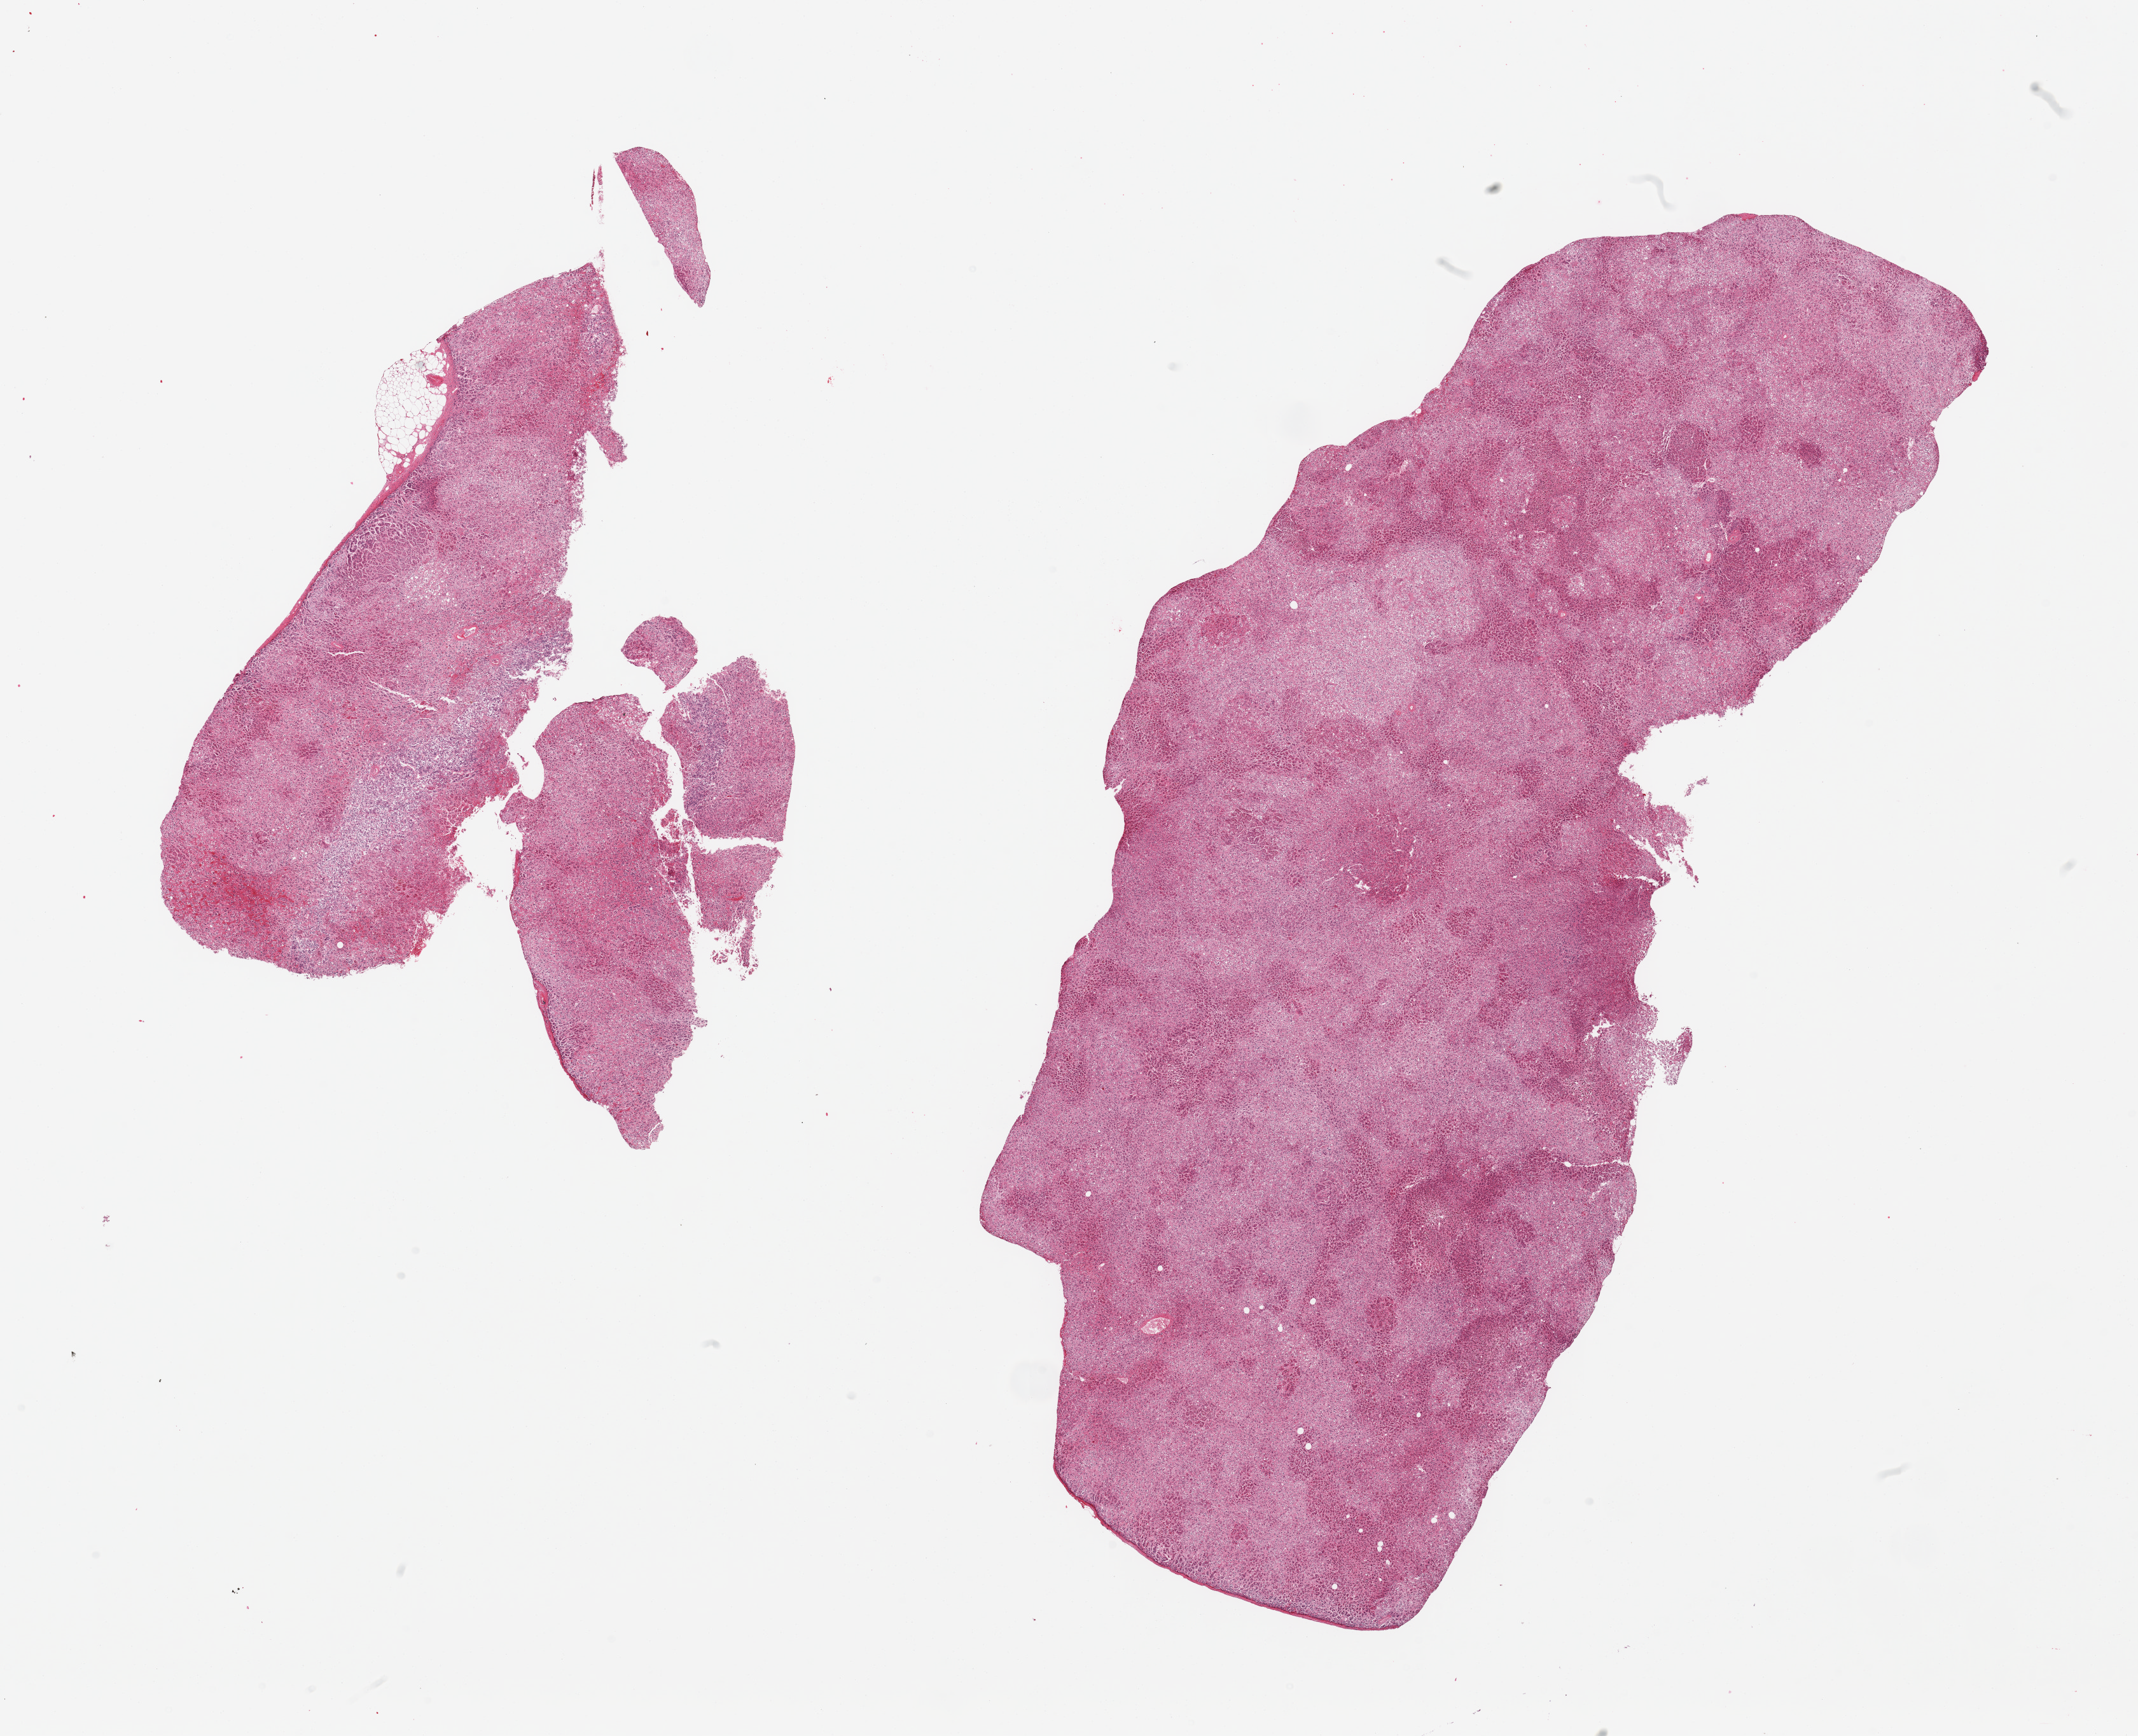
Whole-slide image, H&E stain, shown as a low-resolution overview of the whole scanned area (about 26.6 x 21.6 mm, from a 20x scan); PAXgene-fixed, paraffin-embedded tissue; sampled site (target tissue): adrenal gland; donor tissue sample. Male donor.
* pathologist's review note for this sample: 2 pieces, cortex